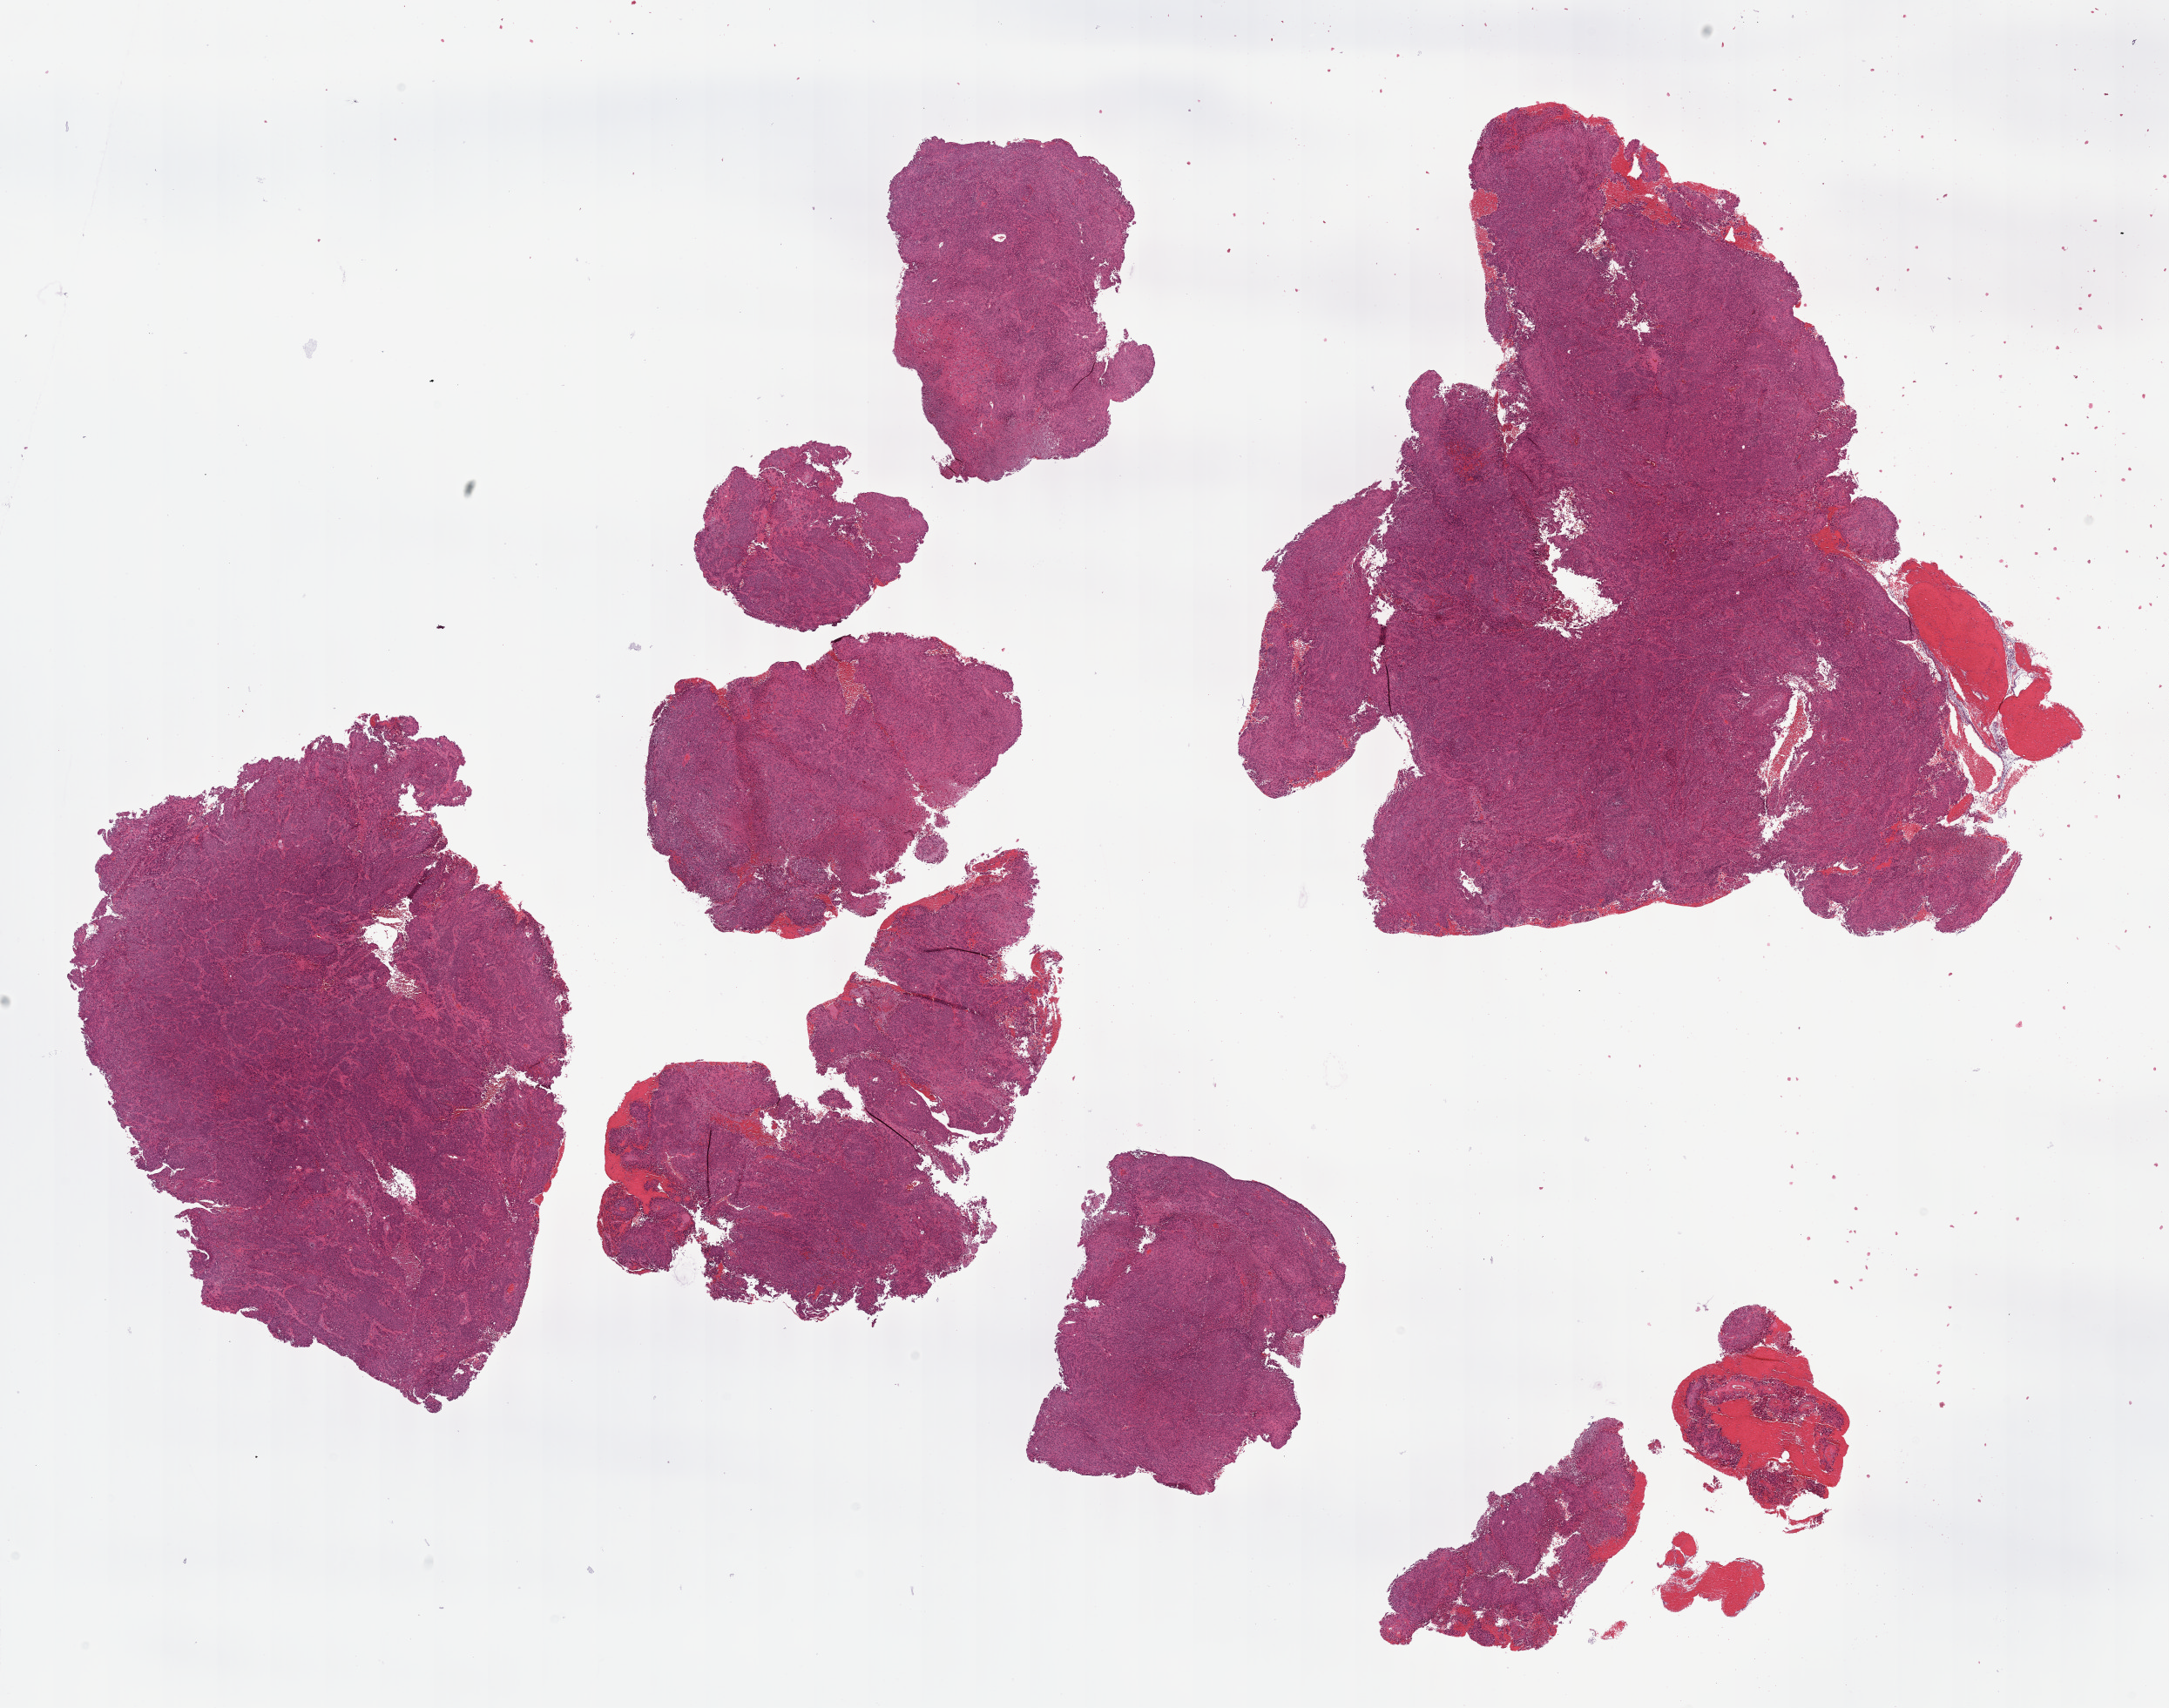
Digitized Hematoxylin and eosin (H&E) stained tissue section (whole slide) — whole scanned area (about 20.1 x 15.8 mm) shown as a low-resolution overview. Formalin-fixed paraffin-embedded (FFPE) diagnostic section. Cervix, primary tumour sample. Female patient; age at initial diagnosis 35 years. Histologic grade: G2 (moderately differentiated).
FIGO stage: IIA. Pathologic diagnosis: Squamous cell carcinoma, NOS (cervix uteri).